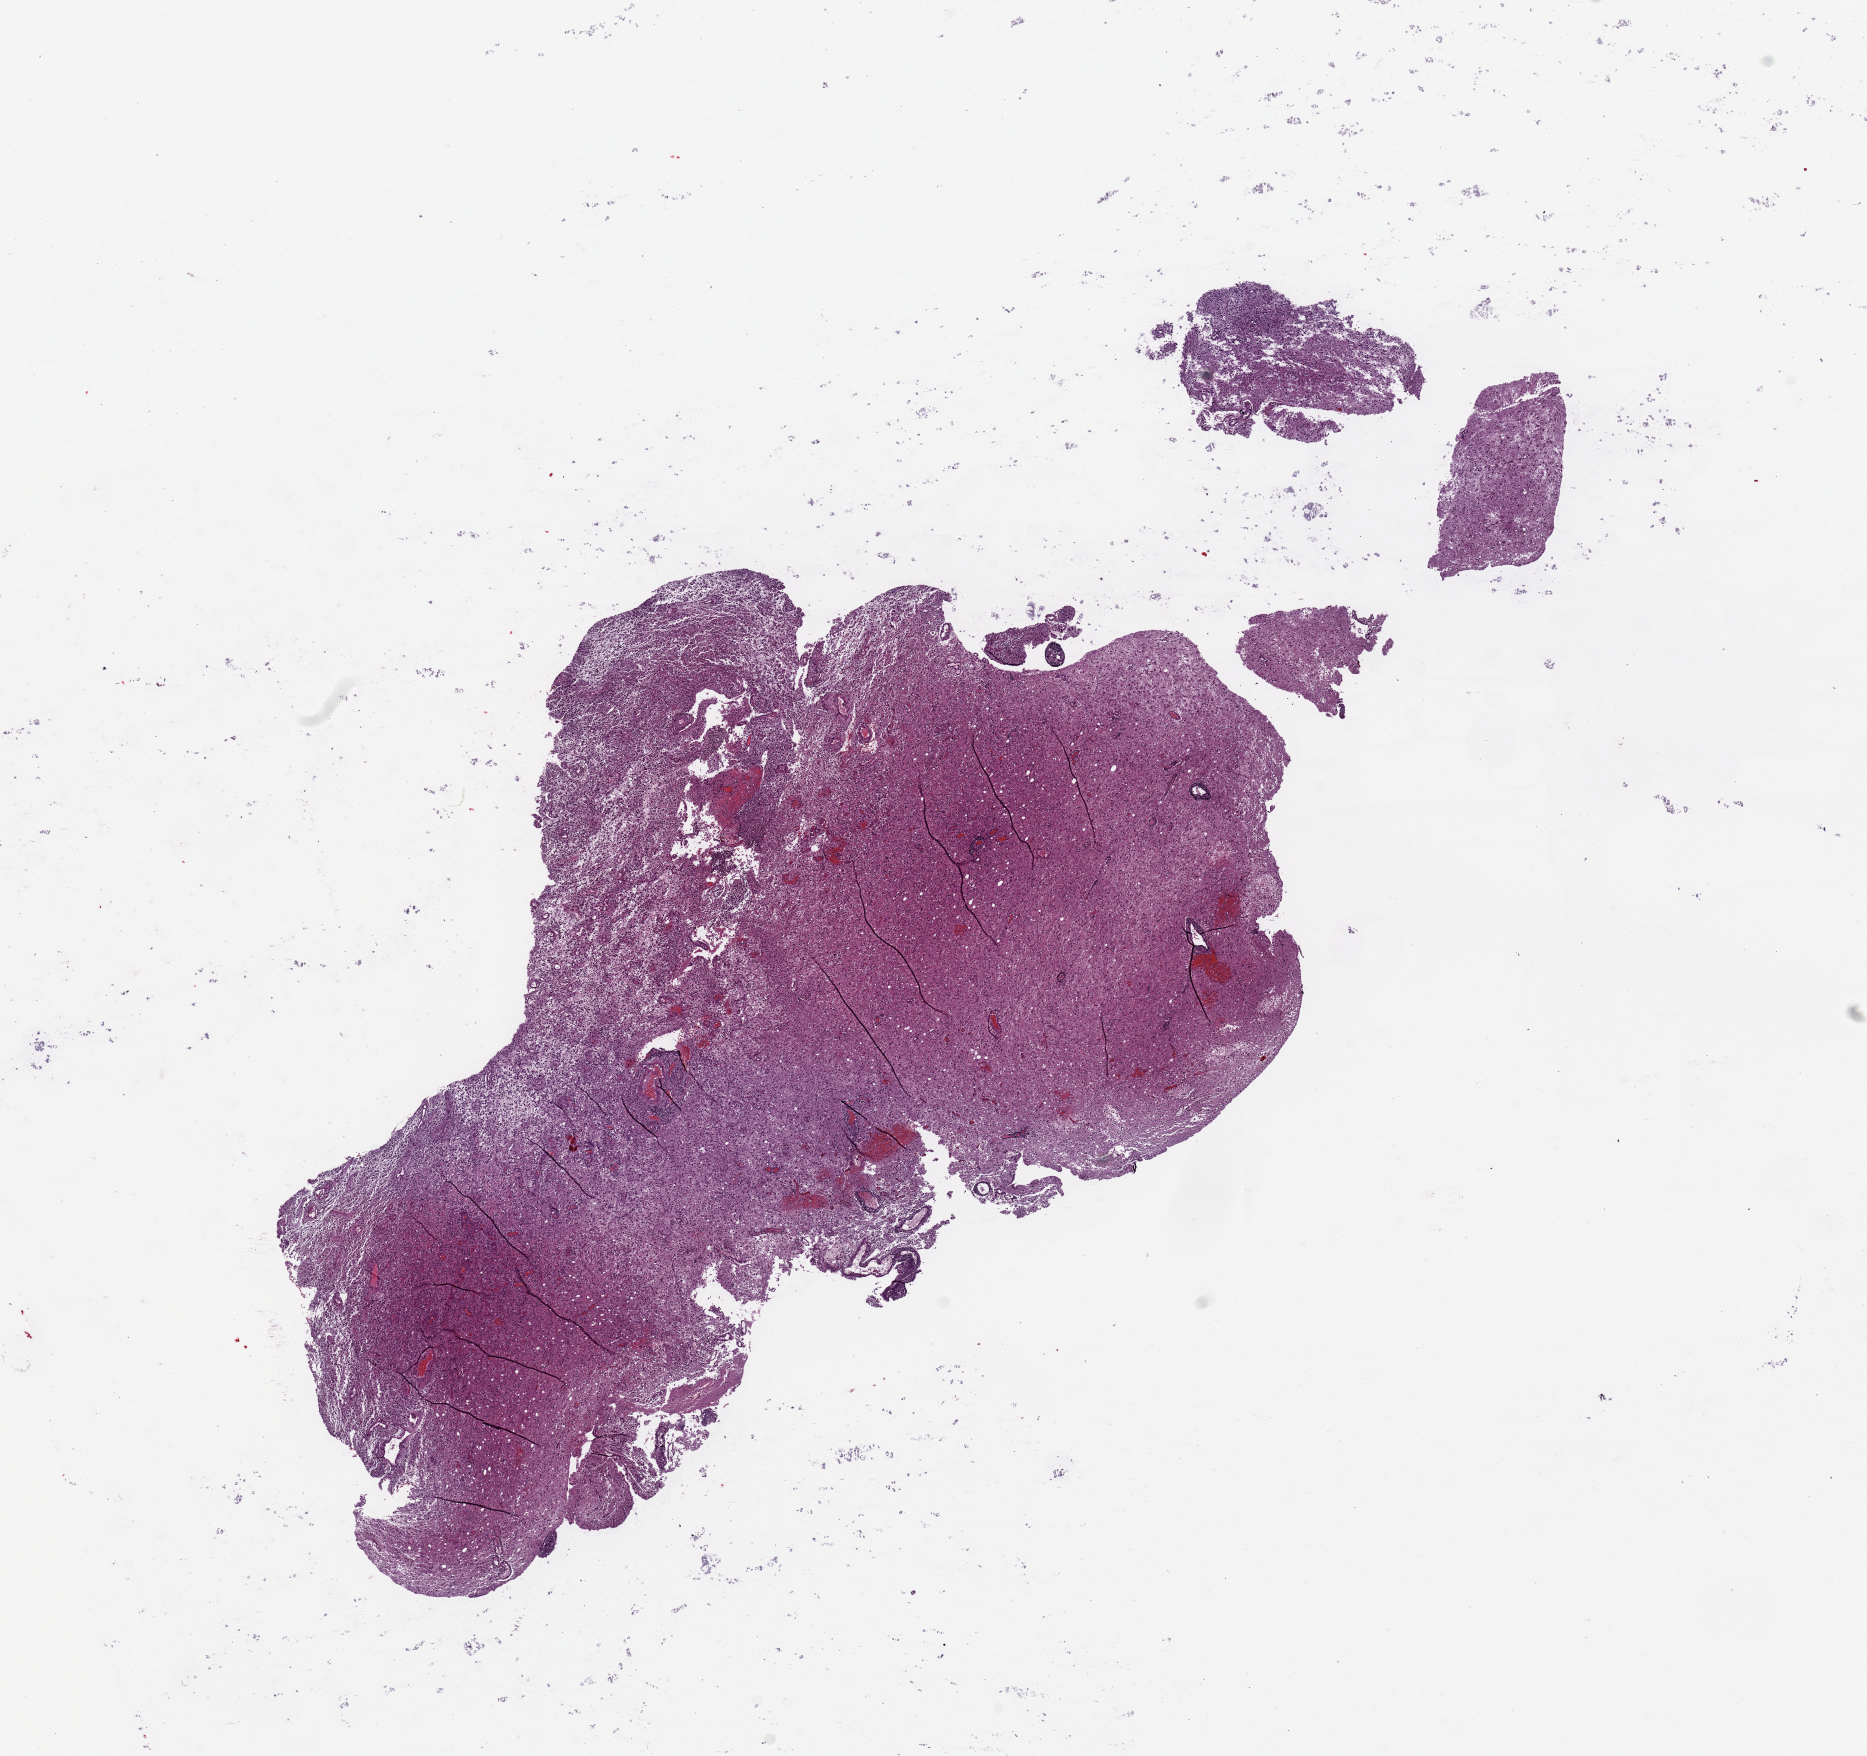
Digitized Hematoxylin and eosin (H&E) stained tissue section (whole slide) — shown as a low-resolution overview of the whole scanned area (about 14.8 x 13.9 mm, slide scanned at 20x), tumour tissue sample, sampled site: brain. Patient: female, age 53 years. Pathologist review of this section (percent, as recorded): tumour nuclei 75%, necrosis 5%.
Primary tumour site (as recorded): temporal lobe. Histologic diagnosis: Glioblastoma.